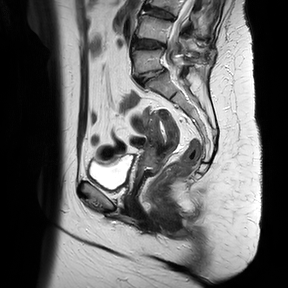
Pelvic MRI for cervical cancer, one sagittal slice; position 21 of 37 along the scan axis; T2-weighted; 1.5 T; TE 100 ms, TR 4174.1 ms; 4 mm slice thickness; 288 × 288 image matrix, field of view 300 × 300 mm. Patient: female, 65 years.
Outlined on this slice (outlined manually by an expert reader):
- uterus and cervix: bounding box <133,108,181,187> (left, top, right, bottom; pixels)